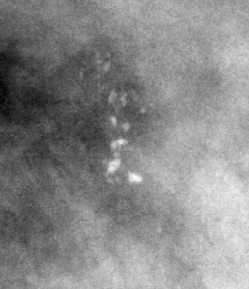
Crop from a digitized film mammogram around one marked abnormality; left breast; MLO view; BI-RADS breast density category 4 (scale 1–4).
- Marked abnormality: calcifications, morphology pleomorphic, distribution clustered; BI-RADS assessment category 4; subtlety rating 4 on a 1 (subtle) to 5 (obvious) scale; pathology (as recorded): malignant.